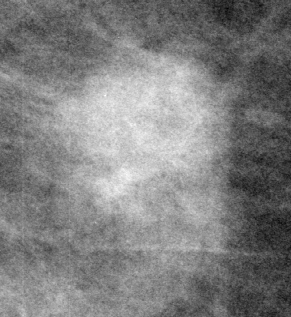
Cropped region of a digitized screen-film mammogram centred on a radiologist-marked abnormality, left breast, MLO view, BI-RADS breast density category 2 (scale 1–4).
- Finding: mass, shape lobulated, margins spiculated; BI-RADS assessment category 5; subtlety rating 5 on a 1 (subtle) to 5 (obvious) scale; pathology result (as recorded, not read from the image): malignant.